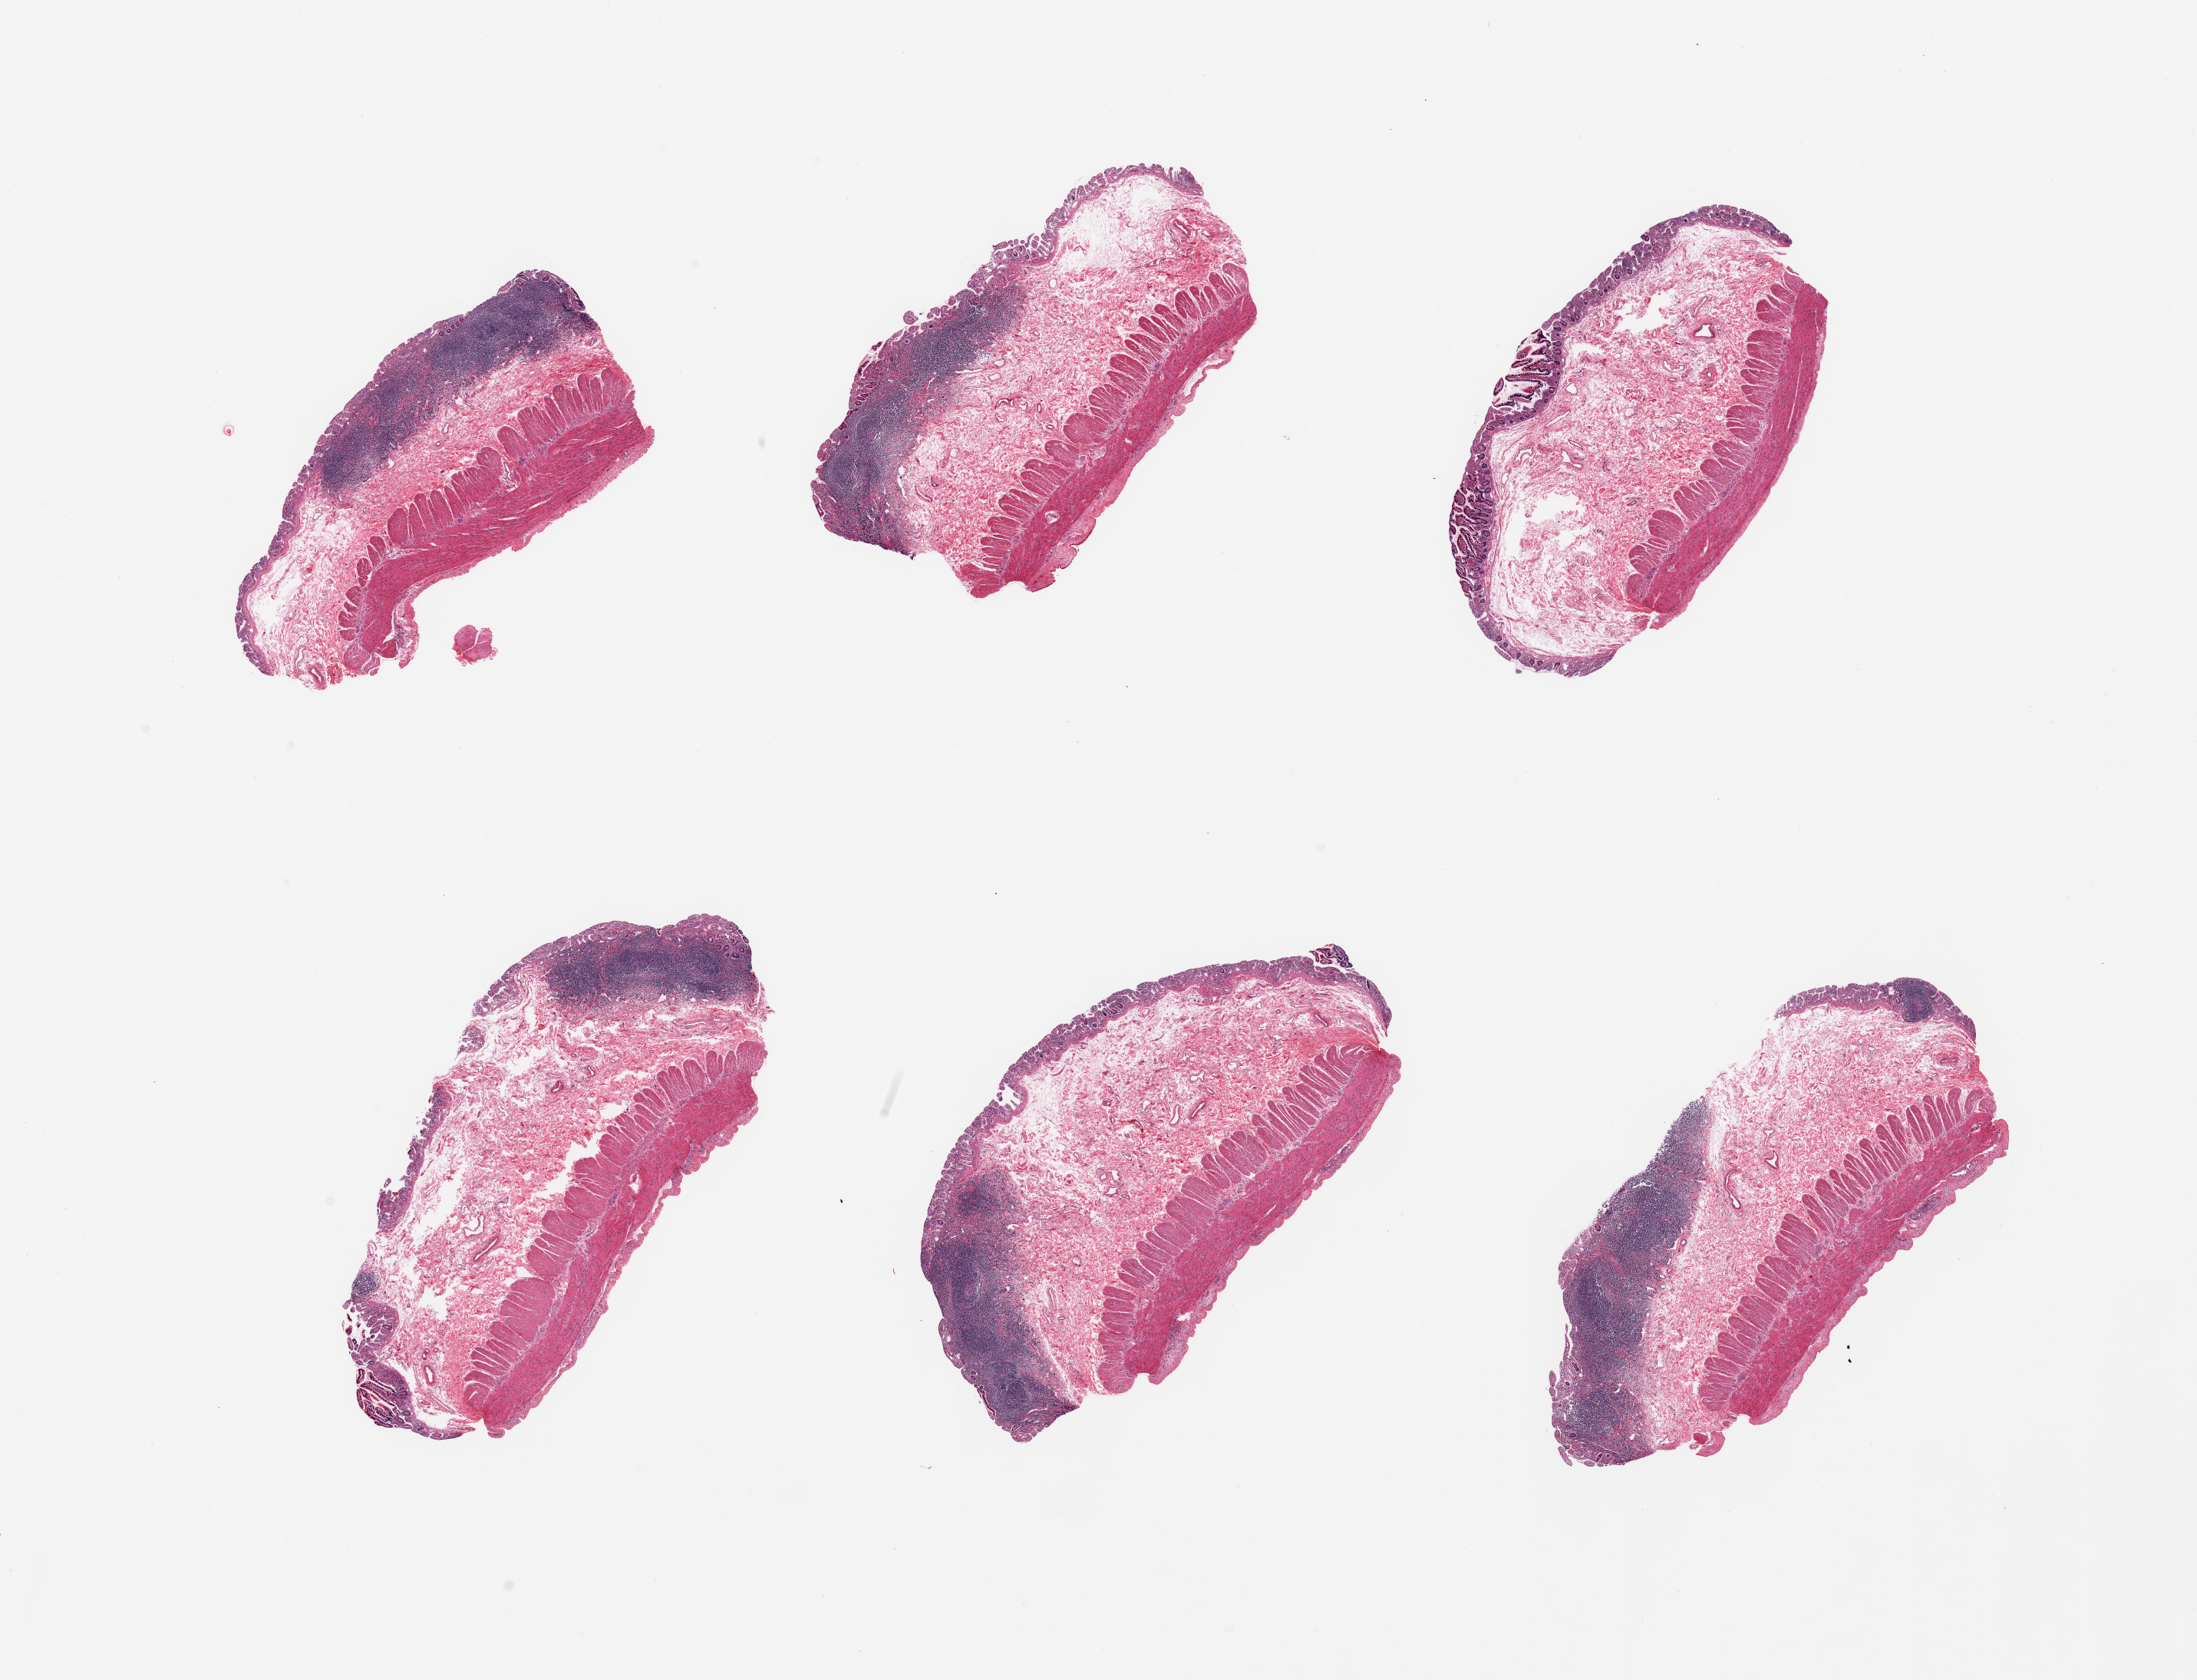
Digitized hematoxylin and eosin (H&E)-stained section, whole scanned area (about 22.6 x 17.3 mm, acquisition: 20x scan) shown as a low-resolution overview. Donor: male.
Specimen: PAXgene-fixed paraffin-embedded (PFPE) section; target tissue: ileum; donor tissue sample.